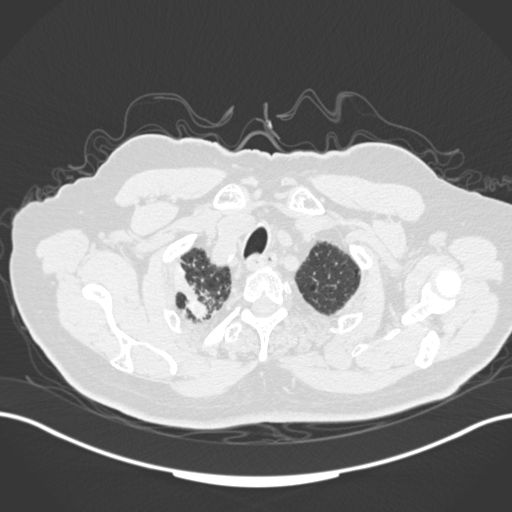
Chest CT, one axial slice. Slice 156 of 205 in the series (ordered by position). 120 kVp. Lung window (W 1500 / L -600 HU). 1 mm slice thickness. 512 × 512 image matrix, field of view 400 × 400 mm. Patient: male, 72 years. Case-level facts recorded for this patient, not image findings: clinical TNM (as recorded): T1a N0 M0.
Structures marked on this image (bounding box drawn by a radiologist):
- lung tumour (recorded histology: squamous cell carcinoma): box from (x=165, y=257) to (x=210, y=323) px